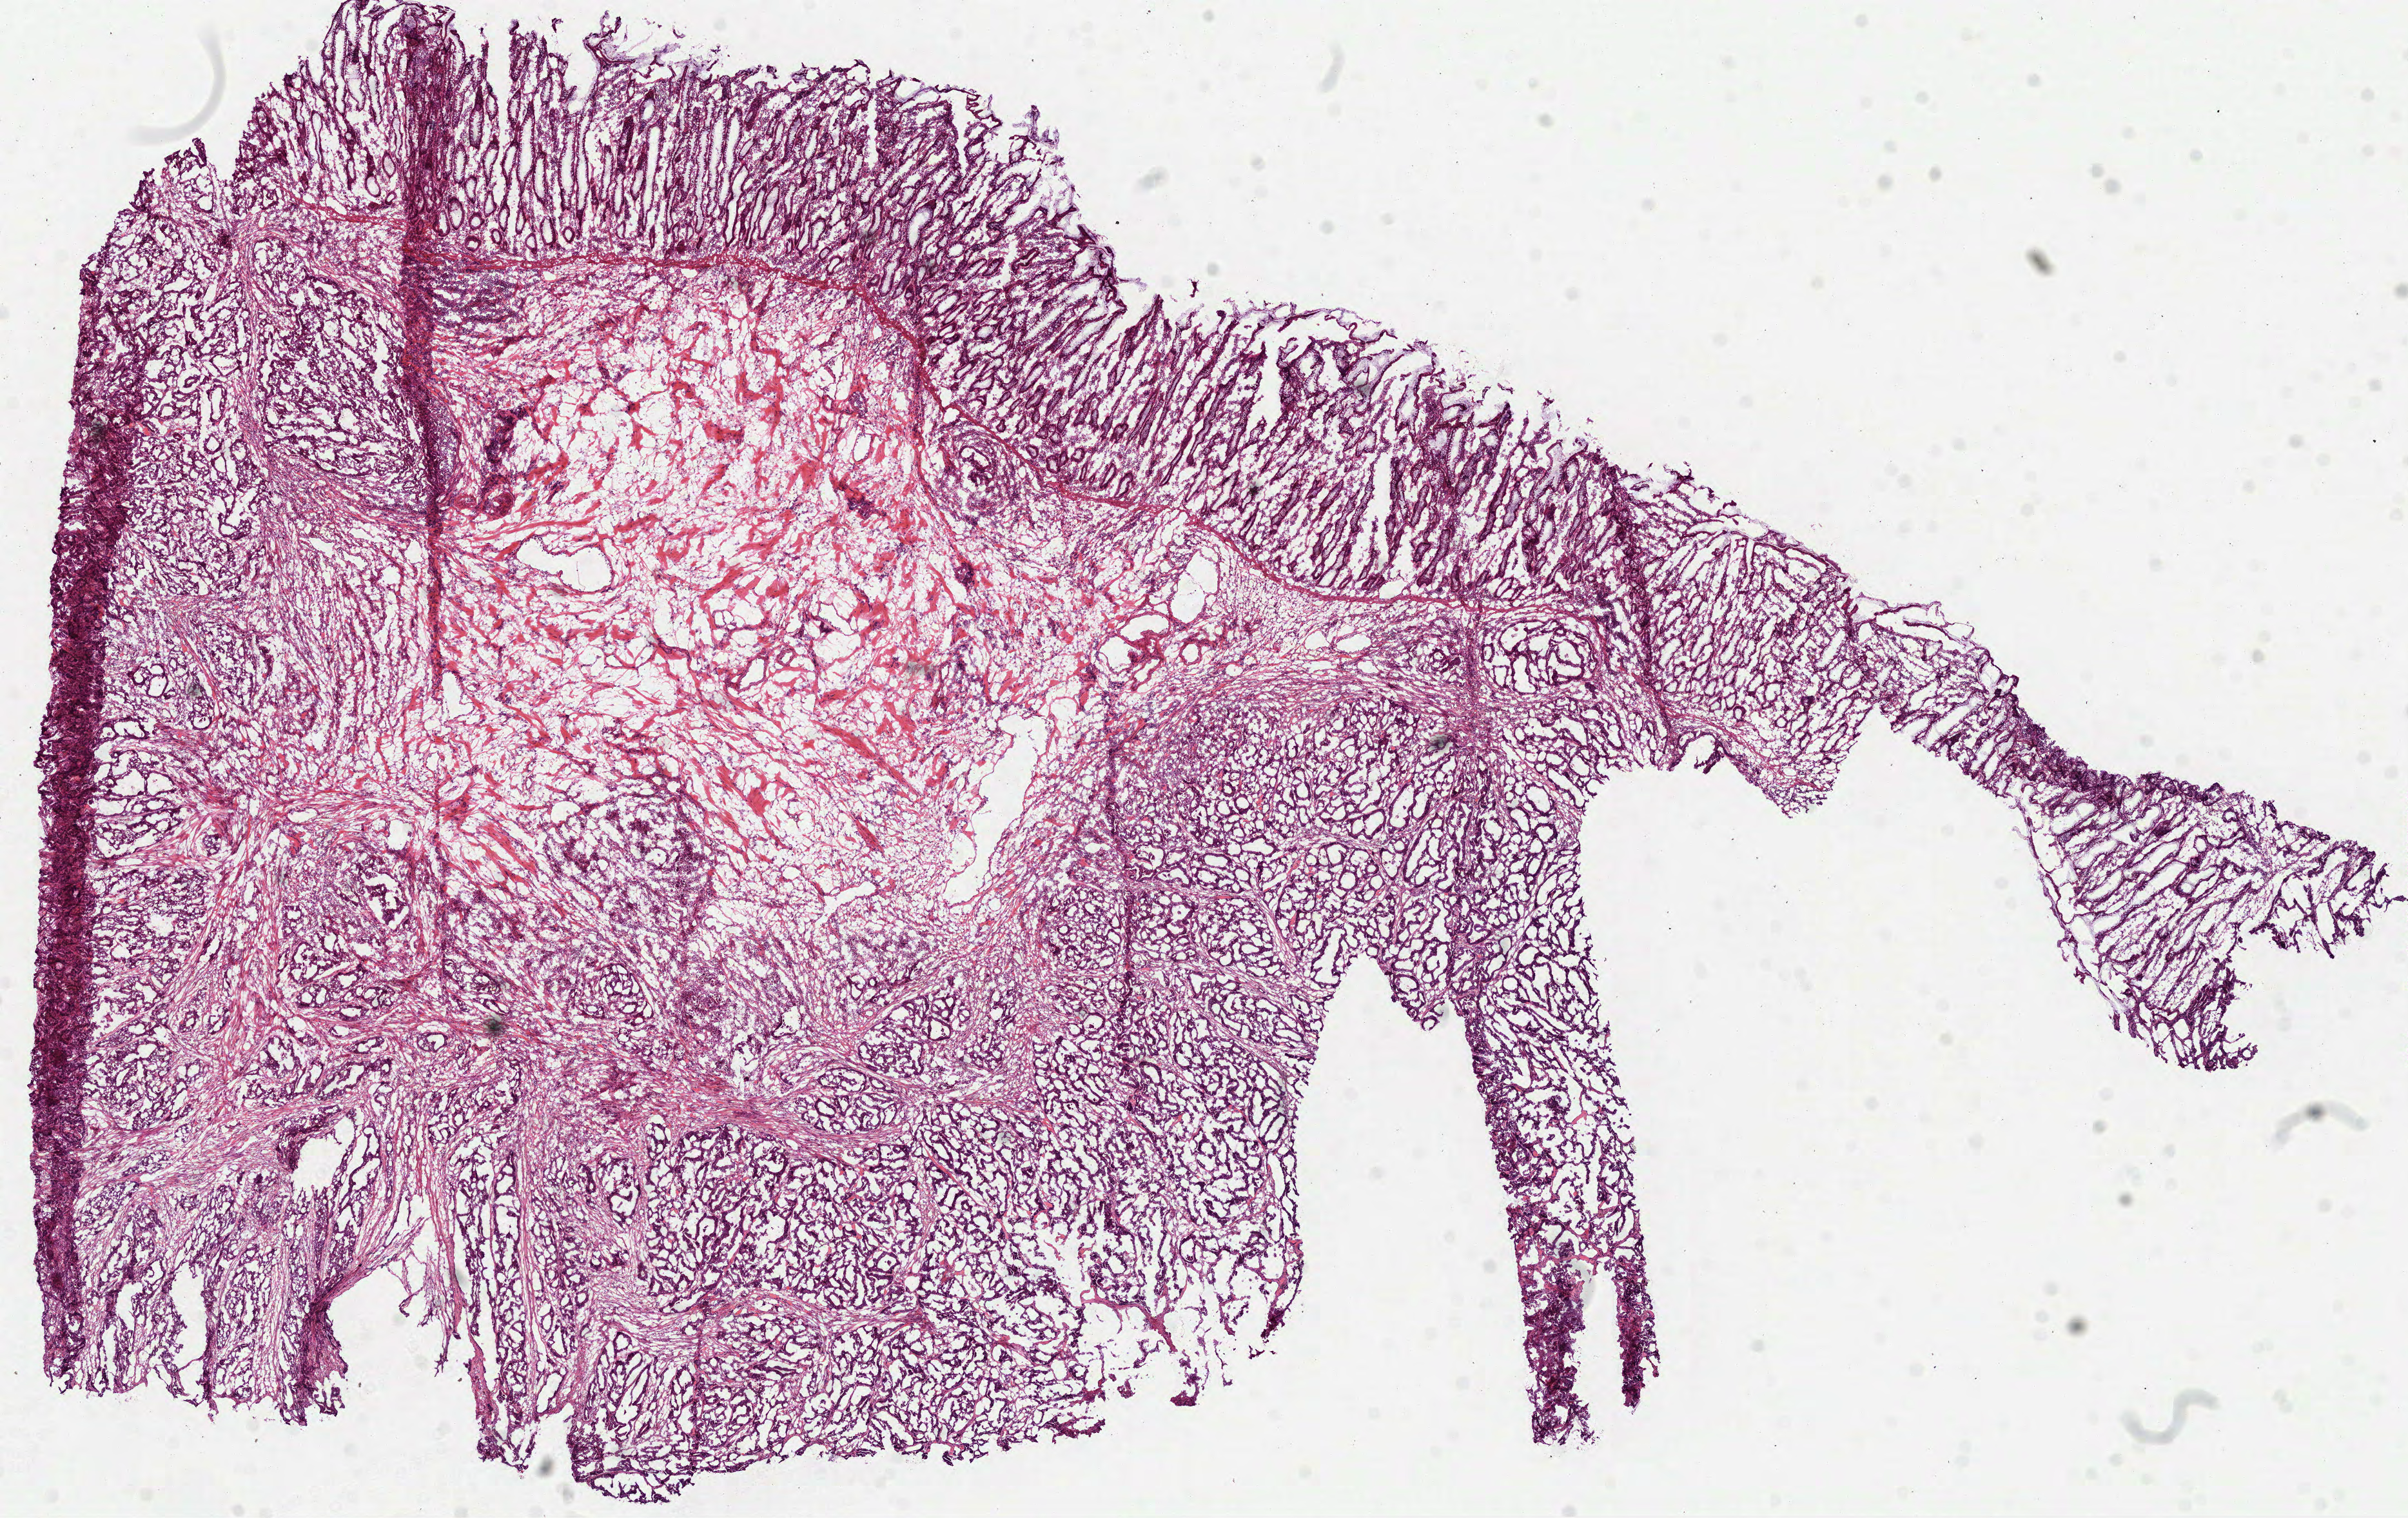
Whole-slide histology image, H&E-stained — whole scanned area (about 15.1 x 9.5 mm) shown as a low-resolution overview; frozen section from the bottom of the tissue portion; colon, primary tumour sample. Male patient.
Histologic diagnosis: Adenocarcinoma, NOS (ascending colon).